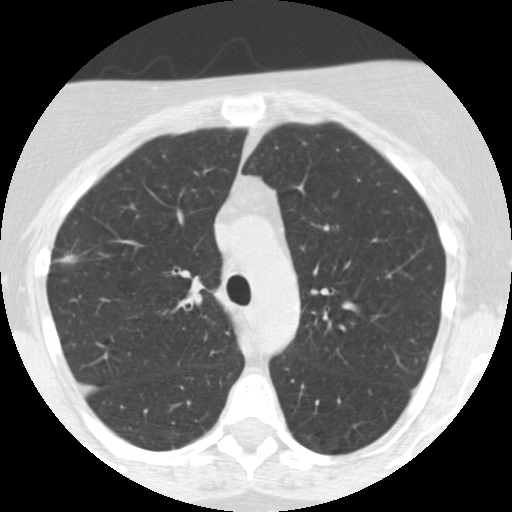
Low-dose screening chest CT, one axial slice; position 177 of 248 along the scan axis; reconstruction kernel STANDARD; lung window (W 1500 / L -600 HU); 2.5 mm slice thickness; 512 × 512 image matrix.
Outlined on this slice (outlined manually by an expert reader):
- lesion 1 (tumor, upper lobe of right lung): bounding box (x1, y1, x2, y2) in pixels: (61, 256, 72, 262)